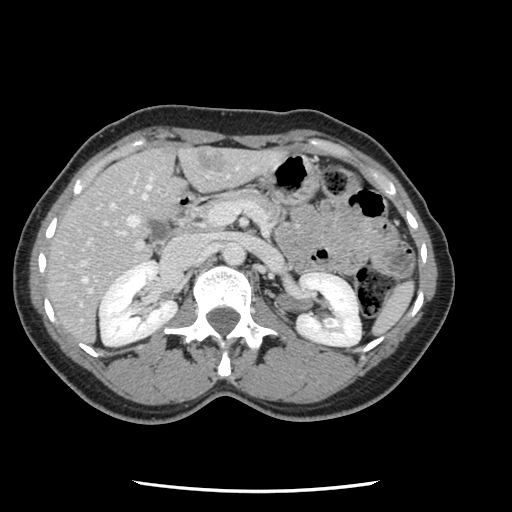
Contrast-enhanced abdominal CT, one axial slice; position 57 of 134 along the scan axis; intravenous contrast given; soft-tissue window (W 400 / L 40 HU); 2.5 mm slice thickness; 512 × 512 image matrix, field of view 330 × 330 mm. Female patient, age 43 years. From the clinical record (not read from this slice): diagnosis: colorectal cancer liver metastases, imaged before liver resection; multiple liver metastases: yes; largest metastasis: 3.4 cm; disease in both lobes: yes.
Structures marked on this image (manually delineated by an expert):
- hepatic veins: bounding box [x1, y1, x2, y2] px = [82, 177, 153, 283]
- liver: [45, 146, 284, 345]
- planned liver remnant (the part of the liver to remain after resection): [46, 146, 182, 324]
- portal vein (with intrahepatic branches): [79, 167, 269, 294]
- liver metastasis: [198, 153, 227, 172]